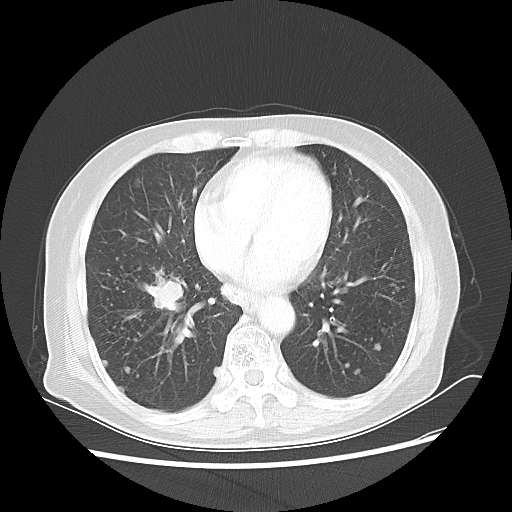
Chest CT, one axial slice. Position 21 of 56 along the scan axis. Reconstruction kernel LUNG. 80 kVp. Lung window (W 1500 / L -600 HU). 512 × 512 image matrix. Patient: female, 68 years. Case-level facts recorded for this patient, not image findings: clinical TNM (as recorded): T1c N3 M0.
Outlined on this slice (rectangle marked by the reading radiologist):
- lung tumour (recorded histology: squamous cell carcinoma): bounding box <139,265,181,321> (left, top, right, bottom; pixels)